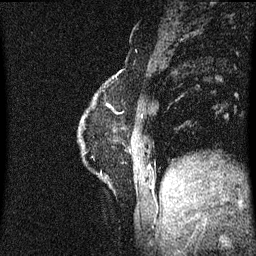
Breast MRI (dynamic contrast-enhanced), one sagittal slice. Position 12 of 60 along the scan axis. Dynamic contrast-enhanced series, image 2 of 3 at this slice position (ordered by acquisition). 1.5 T. TE 4.2 ms, TR 8.4 ms. 256 × 256 image matrix, field of view 200 × 200 mm. Female patient, age 60 years.
Outlined on this slice (semi-automatic segmentation, software-assisted and operator-edited):
- analysis volume of interest (the breast-tissue region the enhancement analysis was run in; not a lesion): bounding box <77,70,123,193> (left, top, right, bottom; pixels)
- tumour enhancement mask (voxels above the 70 % enhancement threshold inside the analysis volume of interest): <82,70,122,121>